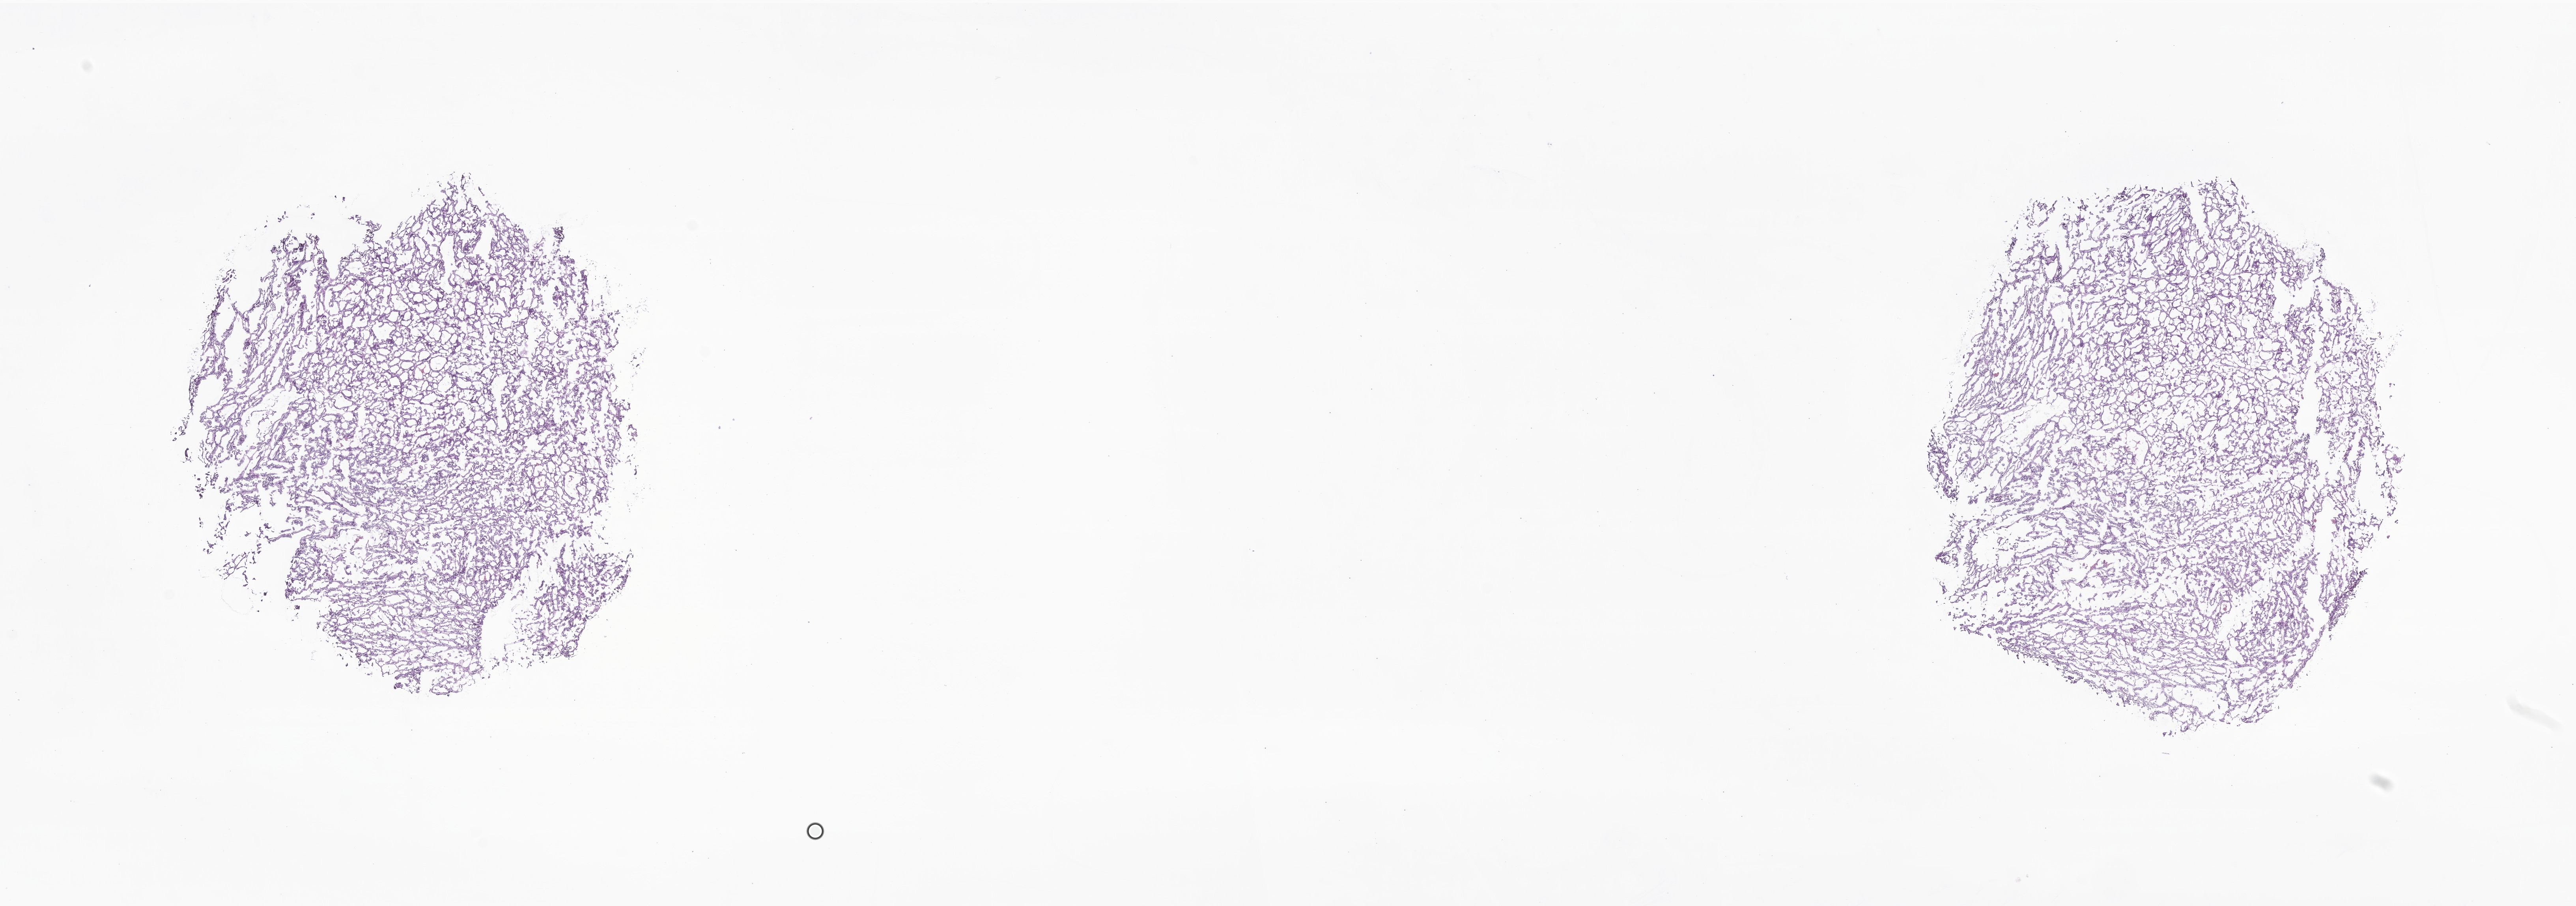
Whole-slide image, haematoxylin and eosin stain of tumor tissue from the thyroid, a low-resolution overview of the entire scanned area, about 27.5 x 9.7 mm. Frozen section (OCT-embedded). Patient female; age 145 months.
* diagnosis (ICD-O-3 morphology term): Papillary carcinoma, NOS